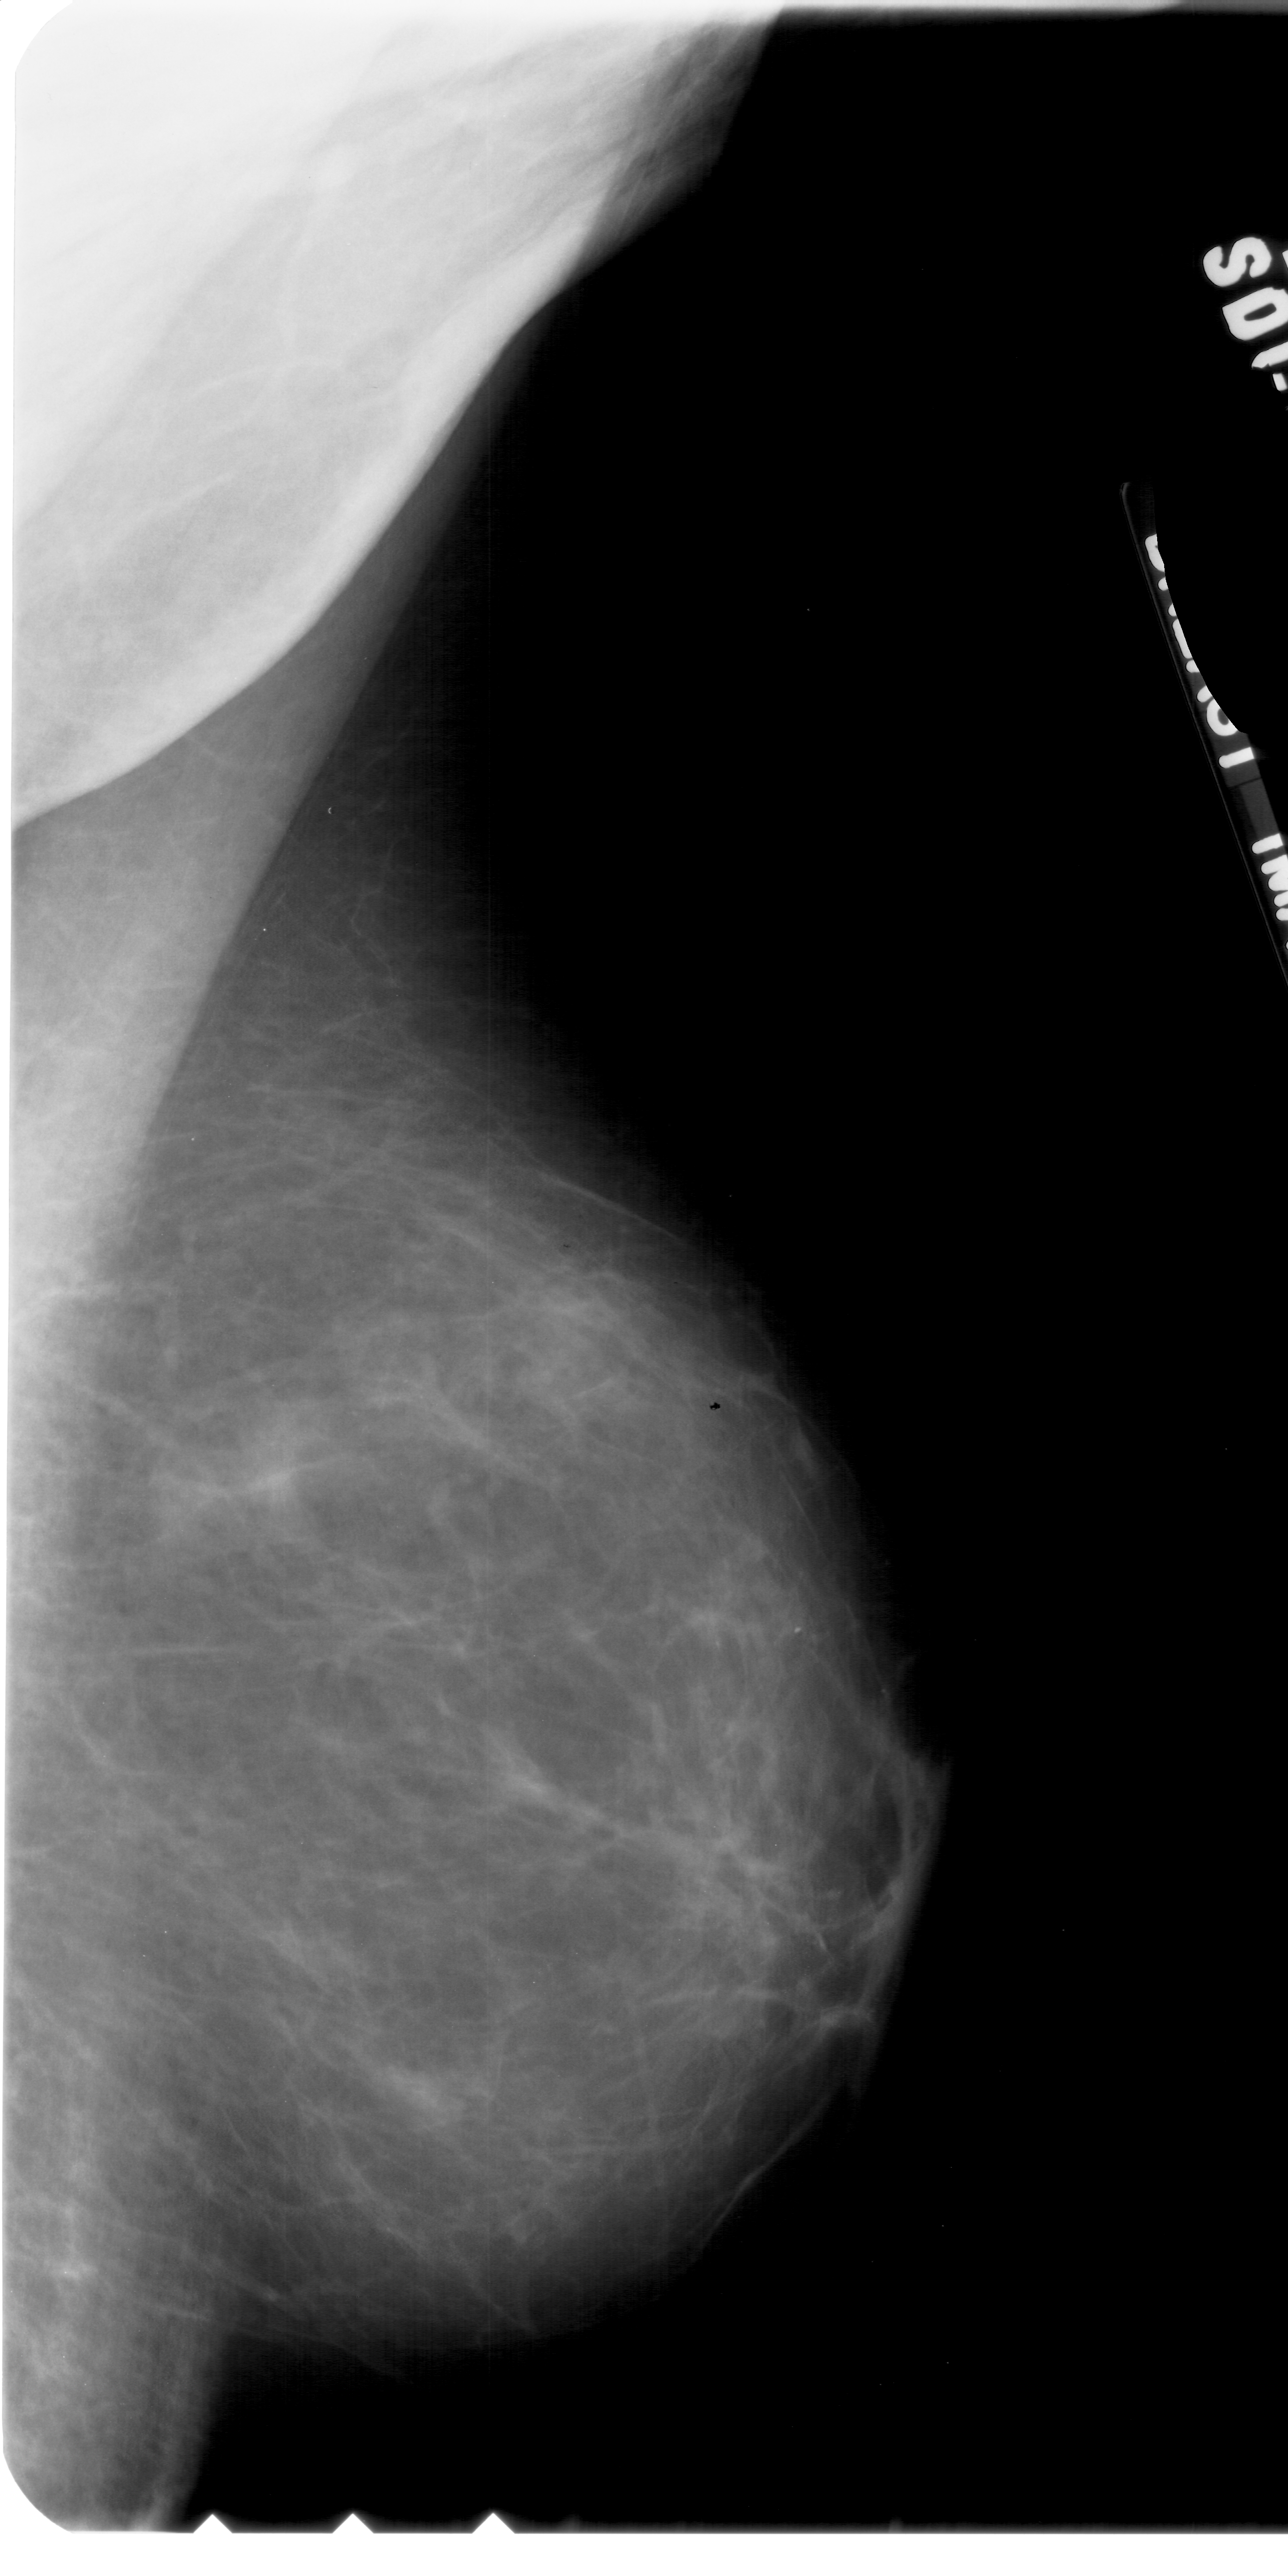
Scanned film-screen mammogram, right breast, MLO view, BI-RADS breast density category 2 (scale 1–4).
- Marked abnormality: calcifications, morphology pleomorphic, distribution clustered; BI-RADS assessment category 4; subtlety rating 2 on a 1 (subtle) to 5 (obvious) scale; pathology result (as recorded, not read from the image): benign.